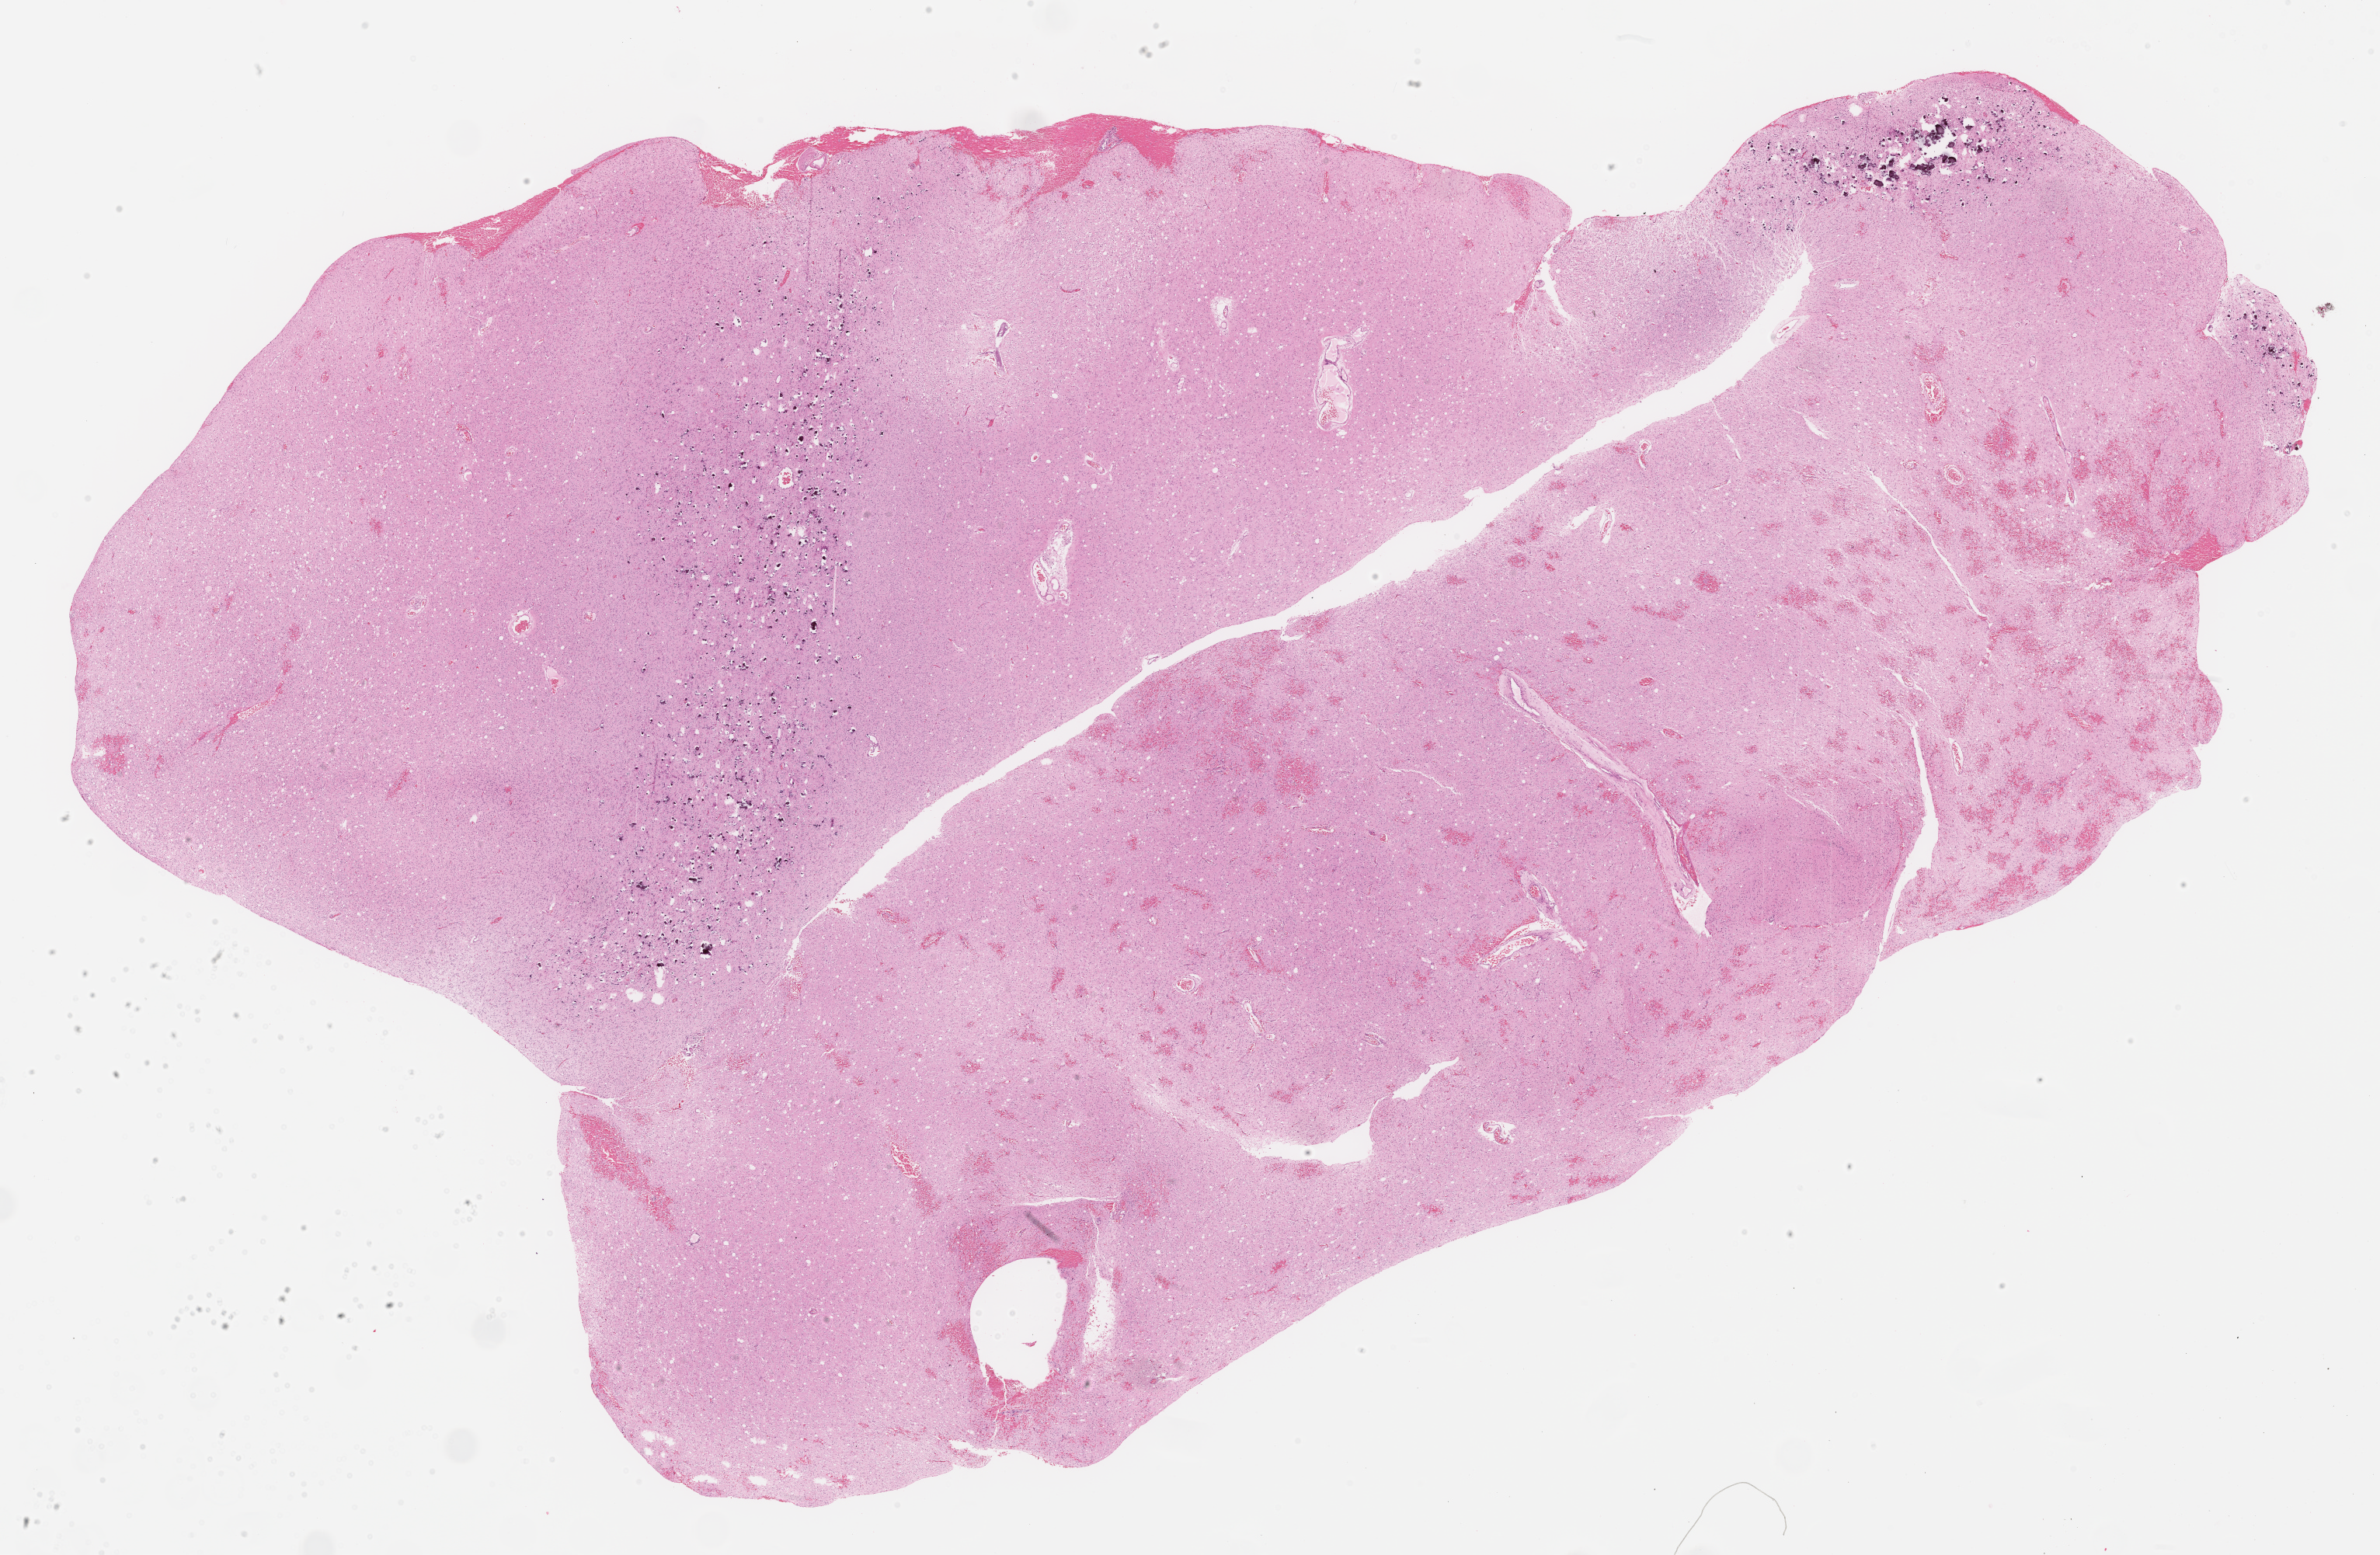
H&E whole-slide image, low-resolution overview of the scanned area, about 24.7 x 16.1 mm (from a 40x scan); formalin-fixed paraffin-embedded (FFPE) diagnostic section; brain, primary tumour sample. Patient: male, age at initial diagnosis 52 years. Histologic grade: G3 (poorly differentiated).
Pathologic diagnosis: Oligodendroglioma, anaplastic. Laterality: left.